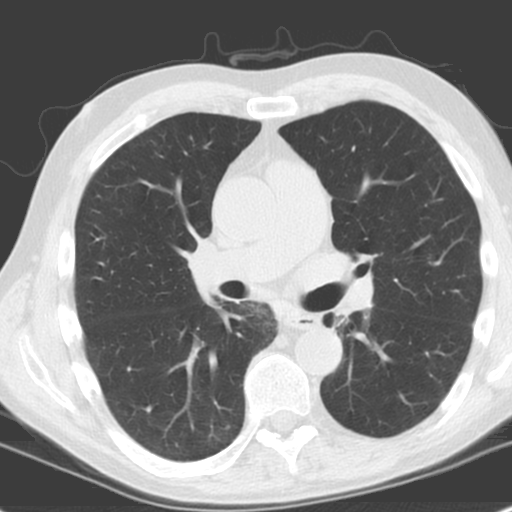
Chest CT (low-dose screening protocol), one axial image. First (baseline) screen. Lung window (W 1500 / L -600 HU). Male, age 61 years at enrolment.
Expert reader's lesion annotation, bounding box <312,307,360,343> (left, top, right, bottom; pixels). No non-calcified nodule or mass ≥4 mm was recorded by the screening reader at this exam. Official screen result: negative screen, minor abnormalities not suspicious for lung cancer. Later outcome: lung cancer diagnosed 1146 days after this screen — squamous cell carcinoma, NOS, left upper lobe, left lower lobe, well differentiated (G1), stage IIB (AJCC 6th edition), 100 mm at pathology.